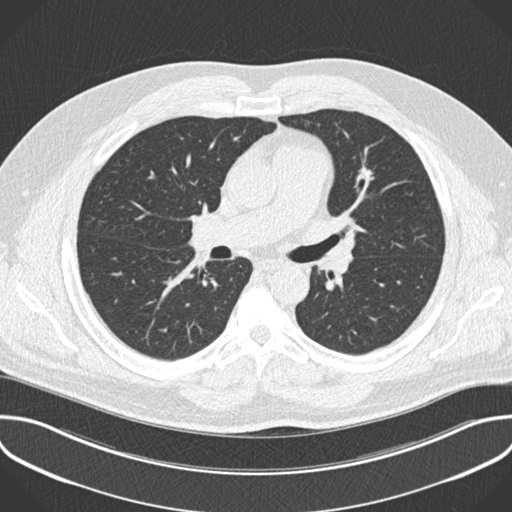
Low-dose screening chest CT, one axial slice. Slice 126 of 201 in the series (ordered by position). 120 kVp. Lung window (W 1500 / L -600 HU). 2 mm slice thickness. 512 × 512 image matrix, field of view 386 × 386 mm.
Structures marked on this image (manually delineated by an expert):
- lesion 1 (tumor, upper lobe of left lung): box from (x=357, y=169) to (x=372, y=185) px